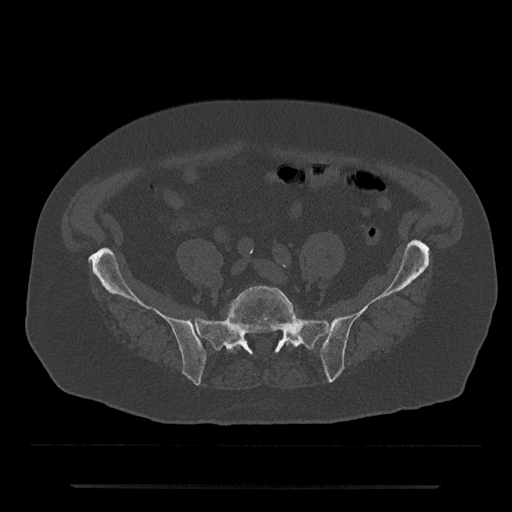
CT including the spine, one axial slice; slice 256 of 797 in the series (ordered by position); reconstruction kernel Br40s/3; 120 kVp; bone window (W 1800 / L 400 HU); 0.5 mm slice thickness; 512 × 512 image matrix, field of view 434 × 434 mm. Patient: male, 80 years. Case-level facts recorded for this patient, not image findings: primary cancer: prostate.
Outlined on this slice (semi-automatic segmentation, software-assisted and operator-edited):
- L5 vertebra: bounding box <226,286,298,353> (left, top, right, bottom; pixels)